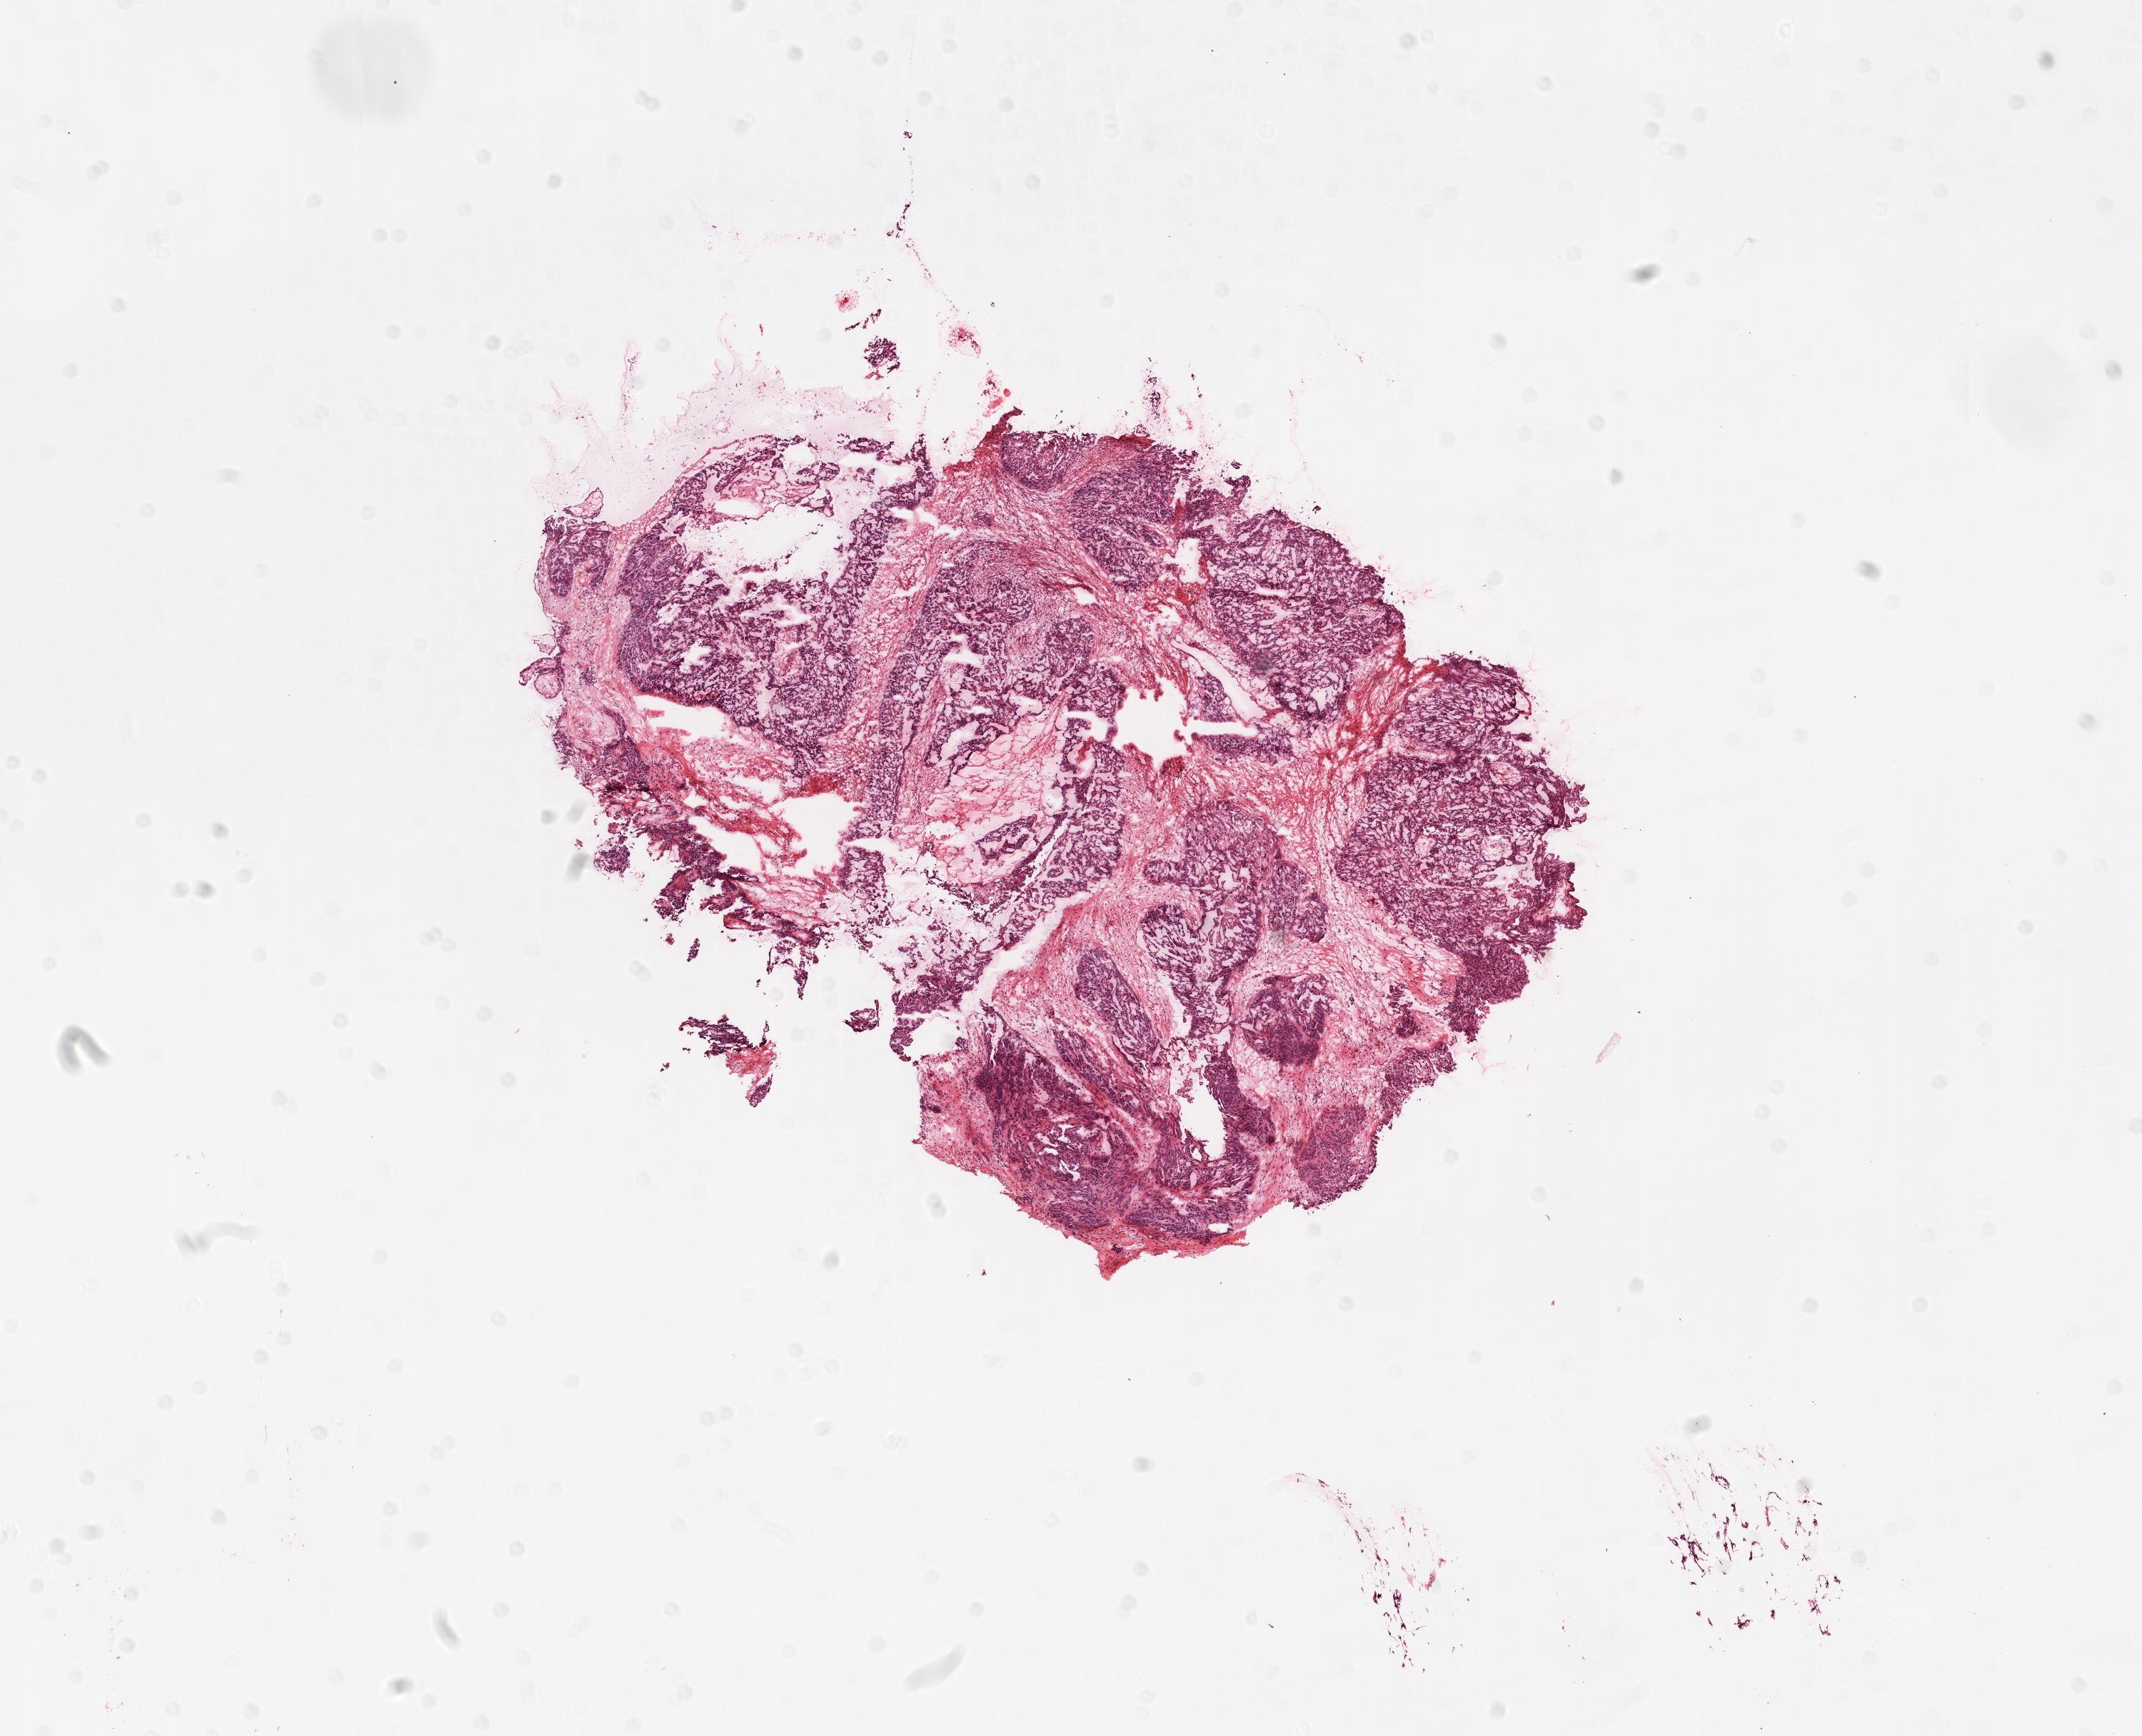
Whole-slide histology image, H&E, a low-resolution overview of the entire scanned area, about 12.0 x 9.8 mm (from a 20x scan), frozen section from the top of the tissue portion, sample: primary tumour, ovary. Female patient; age at initial diagnosis 56 years. Slide review estimates, as recorded: tumour cells 65%, tumour nuclei 75%, normal cells 25%, stromal cells 5%, necrosis 5%.
Histologic diagnosis: Serous cystadenocarcinoma, NOS. FIGO stage: IIIC.